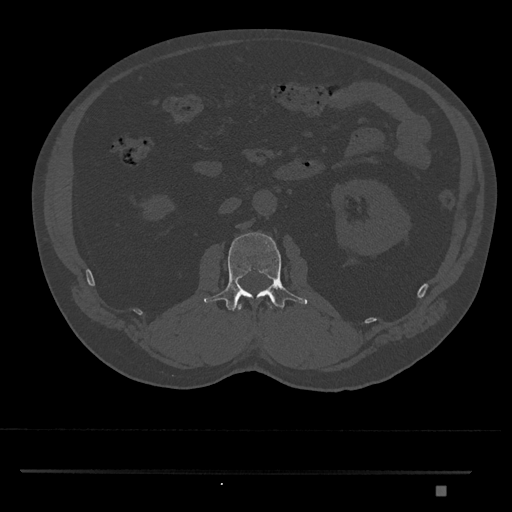
CT including the spine, one axial slice; position 760 of 1134 along the scan axis; 120 kVp; bone window (W 1800 / L 400 HU); 0.5 mm slice thickness; 512 × 512 image matrix, field of view 429 × 429 mm. Patient: male, 65 years. Case-level facts recorded for this patient, not image findings: primary cancer: prostate.
Annotated regions visible in this slice (semi-automatically segmented with operator editing):
- L1 vertebra: bounding box (x1, y1, x2, y2) in pixels: (238, 303, 272, 310)
- L2 vertebra: (204, 232, 308, 311)